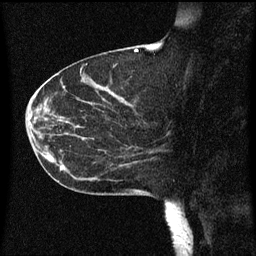
Breast MRI (dynamic contrast-enhanced), one sagittal slice. Position 25 of 60 along the scan axis. Dynamic contrast-enhanced series, image 2 of 3 at this slice position (ordered by acquisition). 1.5 T. TE 4.2 ms, TR 8 ms. 256 × 256 image matrix. Female patient, age 55 years.
Outlined on this slice (semi-automatically segmented with operator editing):
- analysis volume of interest (the breast-tissue region the enhancement analysis was run in; not a lesion): bounding box (x1, y1, x2, y2) in pixels: (46, 124, 151, 183)
- tumour enhancement mask (voxels above the 70 % enhancement threshold inside the analysis volume of interest): (60, 162, 129, 165)